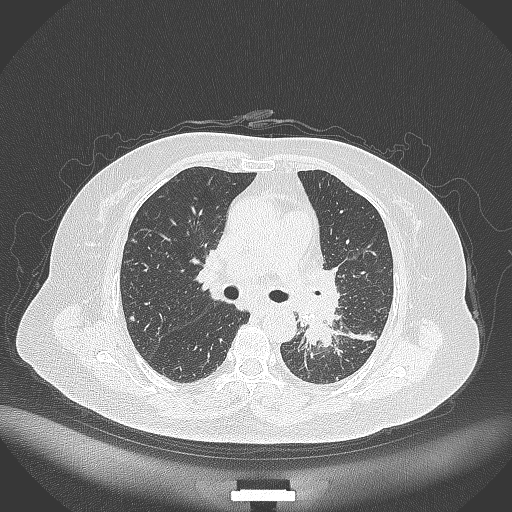
Chest CT, one axial slice; slice 209 of 322 in the series (ordered by position); reconstruction kernel B70f; 120 kVp; lung window (W 1500 / L -600 HU); 1 mm slice thickness; 512 × 512 image matrix, field of view 400 × 400 mm. Female patient, age 69 years. Case-level facts recorded for this patient, not image findings: clinical TNM (as recorded): T2b N3 M1.
Annotated regions visible in this slice (rectangle marked by the reading radiologist):
- lung tumour (recorded histology: adenocarcinoma): box from (x=298, y=317) to (x=334, y=353) px